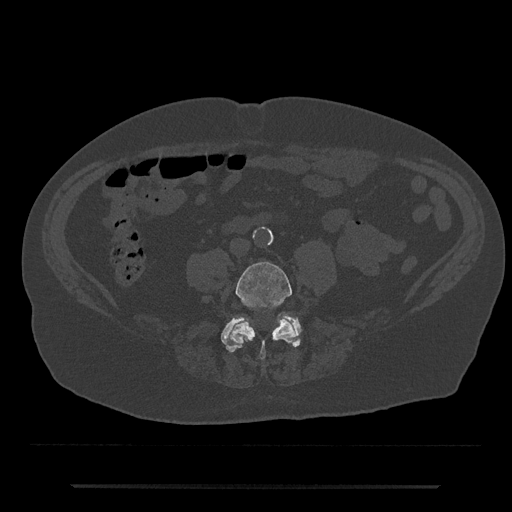
CT including the spine, one axial slice. Position 332 of 797 along the scan axis. Bone window (W 1800 / L 400 HU). 512 × 512 image matrix, field of view 434 × 434 mm. Male patient, age 80 years. Case-level facts recorded for this patient, not image findings: primary cancer: prostate; vertebrae with lytic lesions (as recorded): L1, T11.
Outlined on this slice (semi-automatic segmentation, software-assisted and operator-edited):
- L4 vertebra: box from (x=226, y=262) to (x=296, y=360) px
- L5 vertebra: (x=221, y=314)–(x=302, y=353)